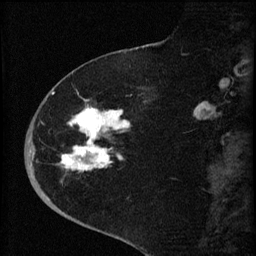
Breast MRI (dynamic contrast-enhanced), one sagittal slice; slice 25 of 60 in the series (ordered by position); dynamic contrast-enhanced series, image 2 of 4 at this slice position (ordered by acquisition); 1.5 T; TE 4.2 ms, TR 8.2 ms; 256 × 256 image matrix, field of view 180 × 180 mm. Female patient, age 71 years.
Annotated regions visible in this slice (semi-automatic segmentation, software-assisted and operator-edited):
- analysis volume of interest (the breast-tissue region the enhancement analysis was run in; not a lesion): box from (x=35, y=75) to (x=149, y=190) px
- tumour enhancement mask (voxels above the 70 % enhancement threshold inside the analysis volume of interest): (x=52, y=89)–(x=130, y=172)